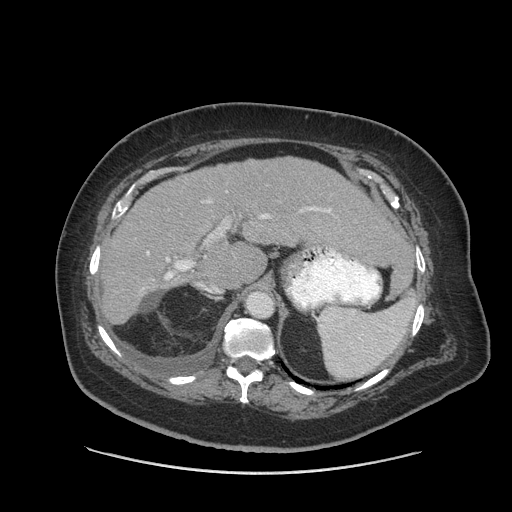
Contrast-enhanced abdominal CT (liver protocol), one axial slice. Position 56 of 91 along the scan axis. Reconstruction kernel STANDARD. Soft-tissue window (W 400 / L 40 HU). 2.5 mm slice thickness. 512 × 512 image matrix, field of view 420 × 420 mm. From the clinical record (not read from this slice): diagnosis: hepatocellular carcinoma (patient treated with transarterial chemoembolisation; whether this scan precedes or follows treatment is not stated here); TNM stage (as recorded): Stage-I; Child-Pugh class: A.
Structures marked on this image (semi-automatically segmented with operator editing):
- liver parenchyma outside the tumour (the mass and vessels are separate outlines, so this box may not span the whole liver): bounding box (x1, y1, x2, y2) in pixels: (100, 158, 403, 324)
- liver vessels: (147, 201, 331, 262)